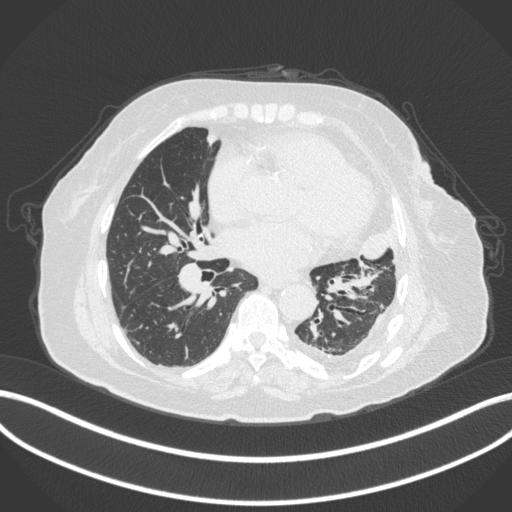
Chest CT, one axial slice. Position 167 of 399 along the scan axis. 120 kVp. Lung window (W 1500 / L -600 HU). 1 mm slice thickness. 512 × 512 image matrix, field of view 400 × 400 mm. Patient: female, 75 years. From the clinical record (not read from this slice): clinical TNM (as recorded): T3 N3 M1.
Annotated regions visible in this slice (rectangle marked by the reading radiologist):
- lung tumour (recorded histology: adenocarcinoma): bounding box [x1, y1, x2, y2] px = [356, 221, 397, 260]